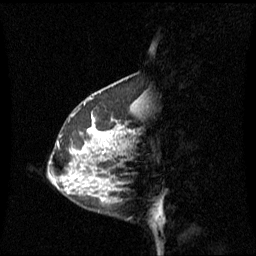
Breast MRI (dynamic contrast-enhanced), one sagittal slice; position 21 of 60 along the scan axis; dynamic contrast-enhanced series, image 2 of 3 at this slice position (ordered by acquisition); 1.5 T; TE 4.2 ms, TR 8.4 ms; 256 × 256 image matrix, field of view 240 × 240 mm. Patient: female, 42 years. From the clinical record (not read from this slice): setting: breast cancer imaged before/during neoadjuvant chemotherapy; receptor status: HR-positive, HER2-negative.
Annotated regions visible in this slice (semi-automatic segmentation, software-assisted and operator-edited):
- analysis volume of interest (the breast-tissue region the enhancement analysis was run in; not a lesion): box from (x=68, y=100) to (x=137, y=201) px
- tumour enhancement mask (voxels above the 70 % enhancement threshold inside the analysis volume of interest): (x=90, y=116)–(x=101, y=139)